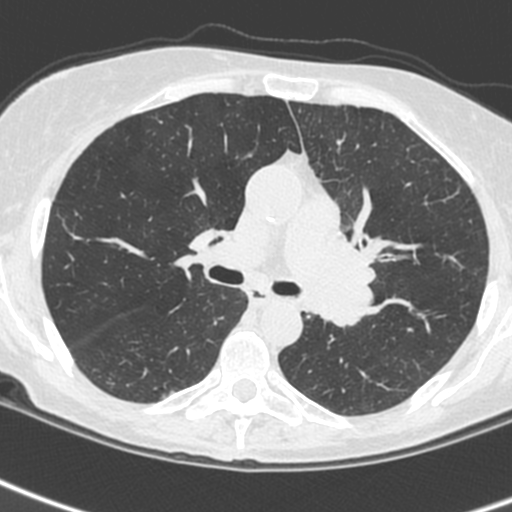
Low-dose screening chest CT, one axial slice. Slice 152 of 242 in the series (ordered by position). Lung window (W 1500 / L -600 HU). 1.3 mm slice thickness. 512 × 512 image matrix.
Structures marked on this image (expert manual segmentation):
- lesion 3 (tumor, upper lobe of left lung): bounding box <307,222,376,327> (left, top, right, bottom; pixels)